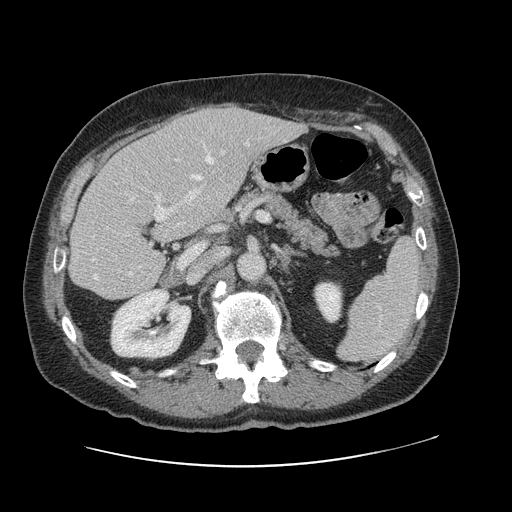
Contrast-enhanced abdominal CT, one axial slice. Slice 61 of 138 in the series (ordered by position). 120 kVp. Intravenous contrast given. Soft-tissue window (W 400 / L 40 HU). 2.5 mm slice thickness. 512 × 512 image matrix. Male patient, age 71 years. Case-level facts recorded for this patient, not image findings: diagnosis: colorectal cancer liver metastases, imaged before liver resection; multiple liver metastases: no; largest metastasis: 3.3 cm.
Structures marked on this image (outlined manually by an expert reader):
- hepatic veins: bounding box [x1, y1, x2, y2] px = [92, 154, 227, 280]
- liver: [71, 106, 302, 299]
- planned liver remnant (the part of the liver to remain after resection): [71, 144, 203, 299]
- portal vein (with intrahepatic branches): [154, 142, 249, 221]